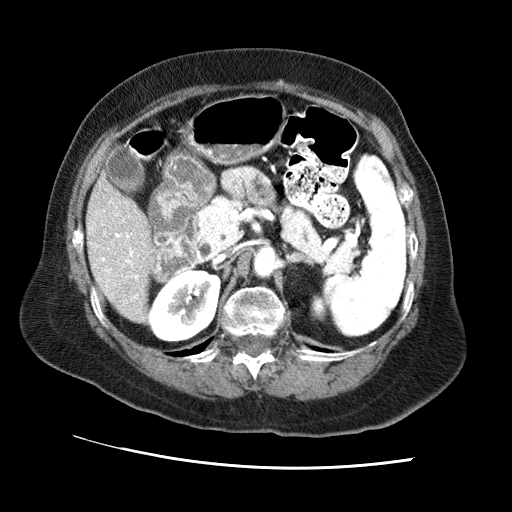
Contrast-enhanced abdominal CT (liver protocol), one axial slice. Position 26 of 65 along the scan axis. Reconstruction kernel STANDARD. 120 kVp. Soft-tissue window (W 400 / L 40 HU). 2.5 mm slice thickness. 512 × 512 image matrix. From the clinical record (not read from this slice): diagnosis: hepatocellular carcinoma (patient treated with transarterial chemoembolisation; whether this scan precedes or follows treatment is not stated here); TNM stage (as recorded): Stage-II; Child-Pugh class: A; tumour differentiation: no biopsy; tumour nodularity: multinodular.
Annotated regions visible in this slice (semi-automatically segmented with operator editing):
- liver parenchyma outside the tumour (the mass and vessels are separate outlines, so this box may not span the whole liver): box from (x=86, y=173) to (x=154, y=321) px
- liver vessels: (x=89, y=201)–(x=139, y=298)